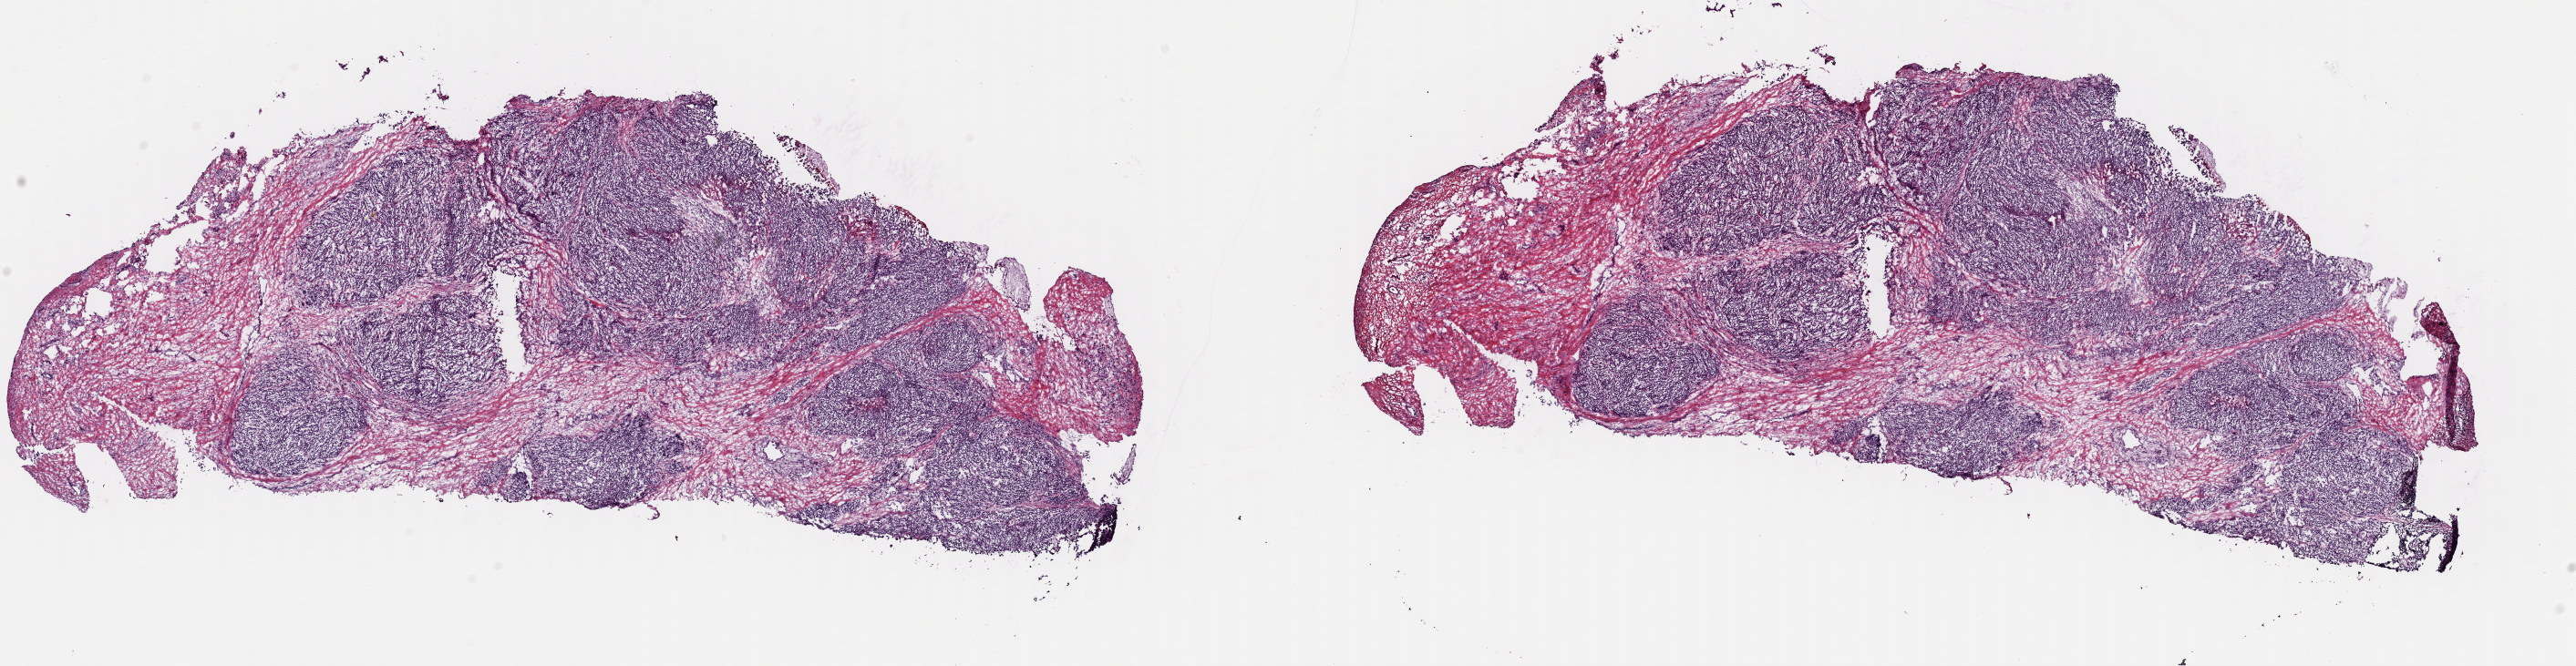
Whole-slide histology image, H&E-stained — whole scanned area (about 22.3 x 5.8 mm) shown as a low-resolution overview; frozen section from the top of the tissue portion; metastatic tumour sample, sampled site: lymph node. Female, age 78 years at initial diagnosis. Slide review estimates, as recorded: tumour cells 80%, tumour nuclei 85%, normal cells 0%, stromal cells 20%, necrosis 0%. Inflammatory infiltration, as recorded: lymphocyte infiltration 0%, monocyte infiltration 0%, neutrophil infiltration 0%.
This section: metastatic tumour tissue. Patient diagnosis: Malignant melanoma, NOS.